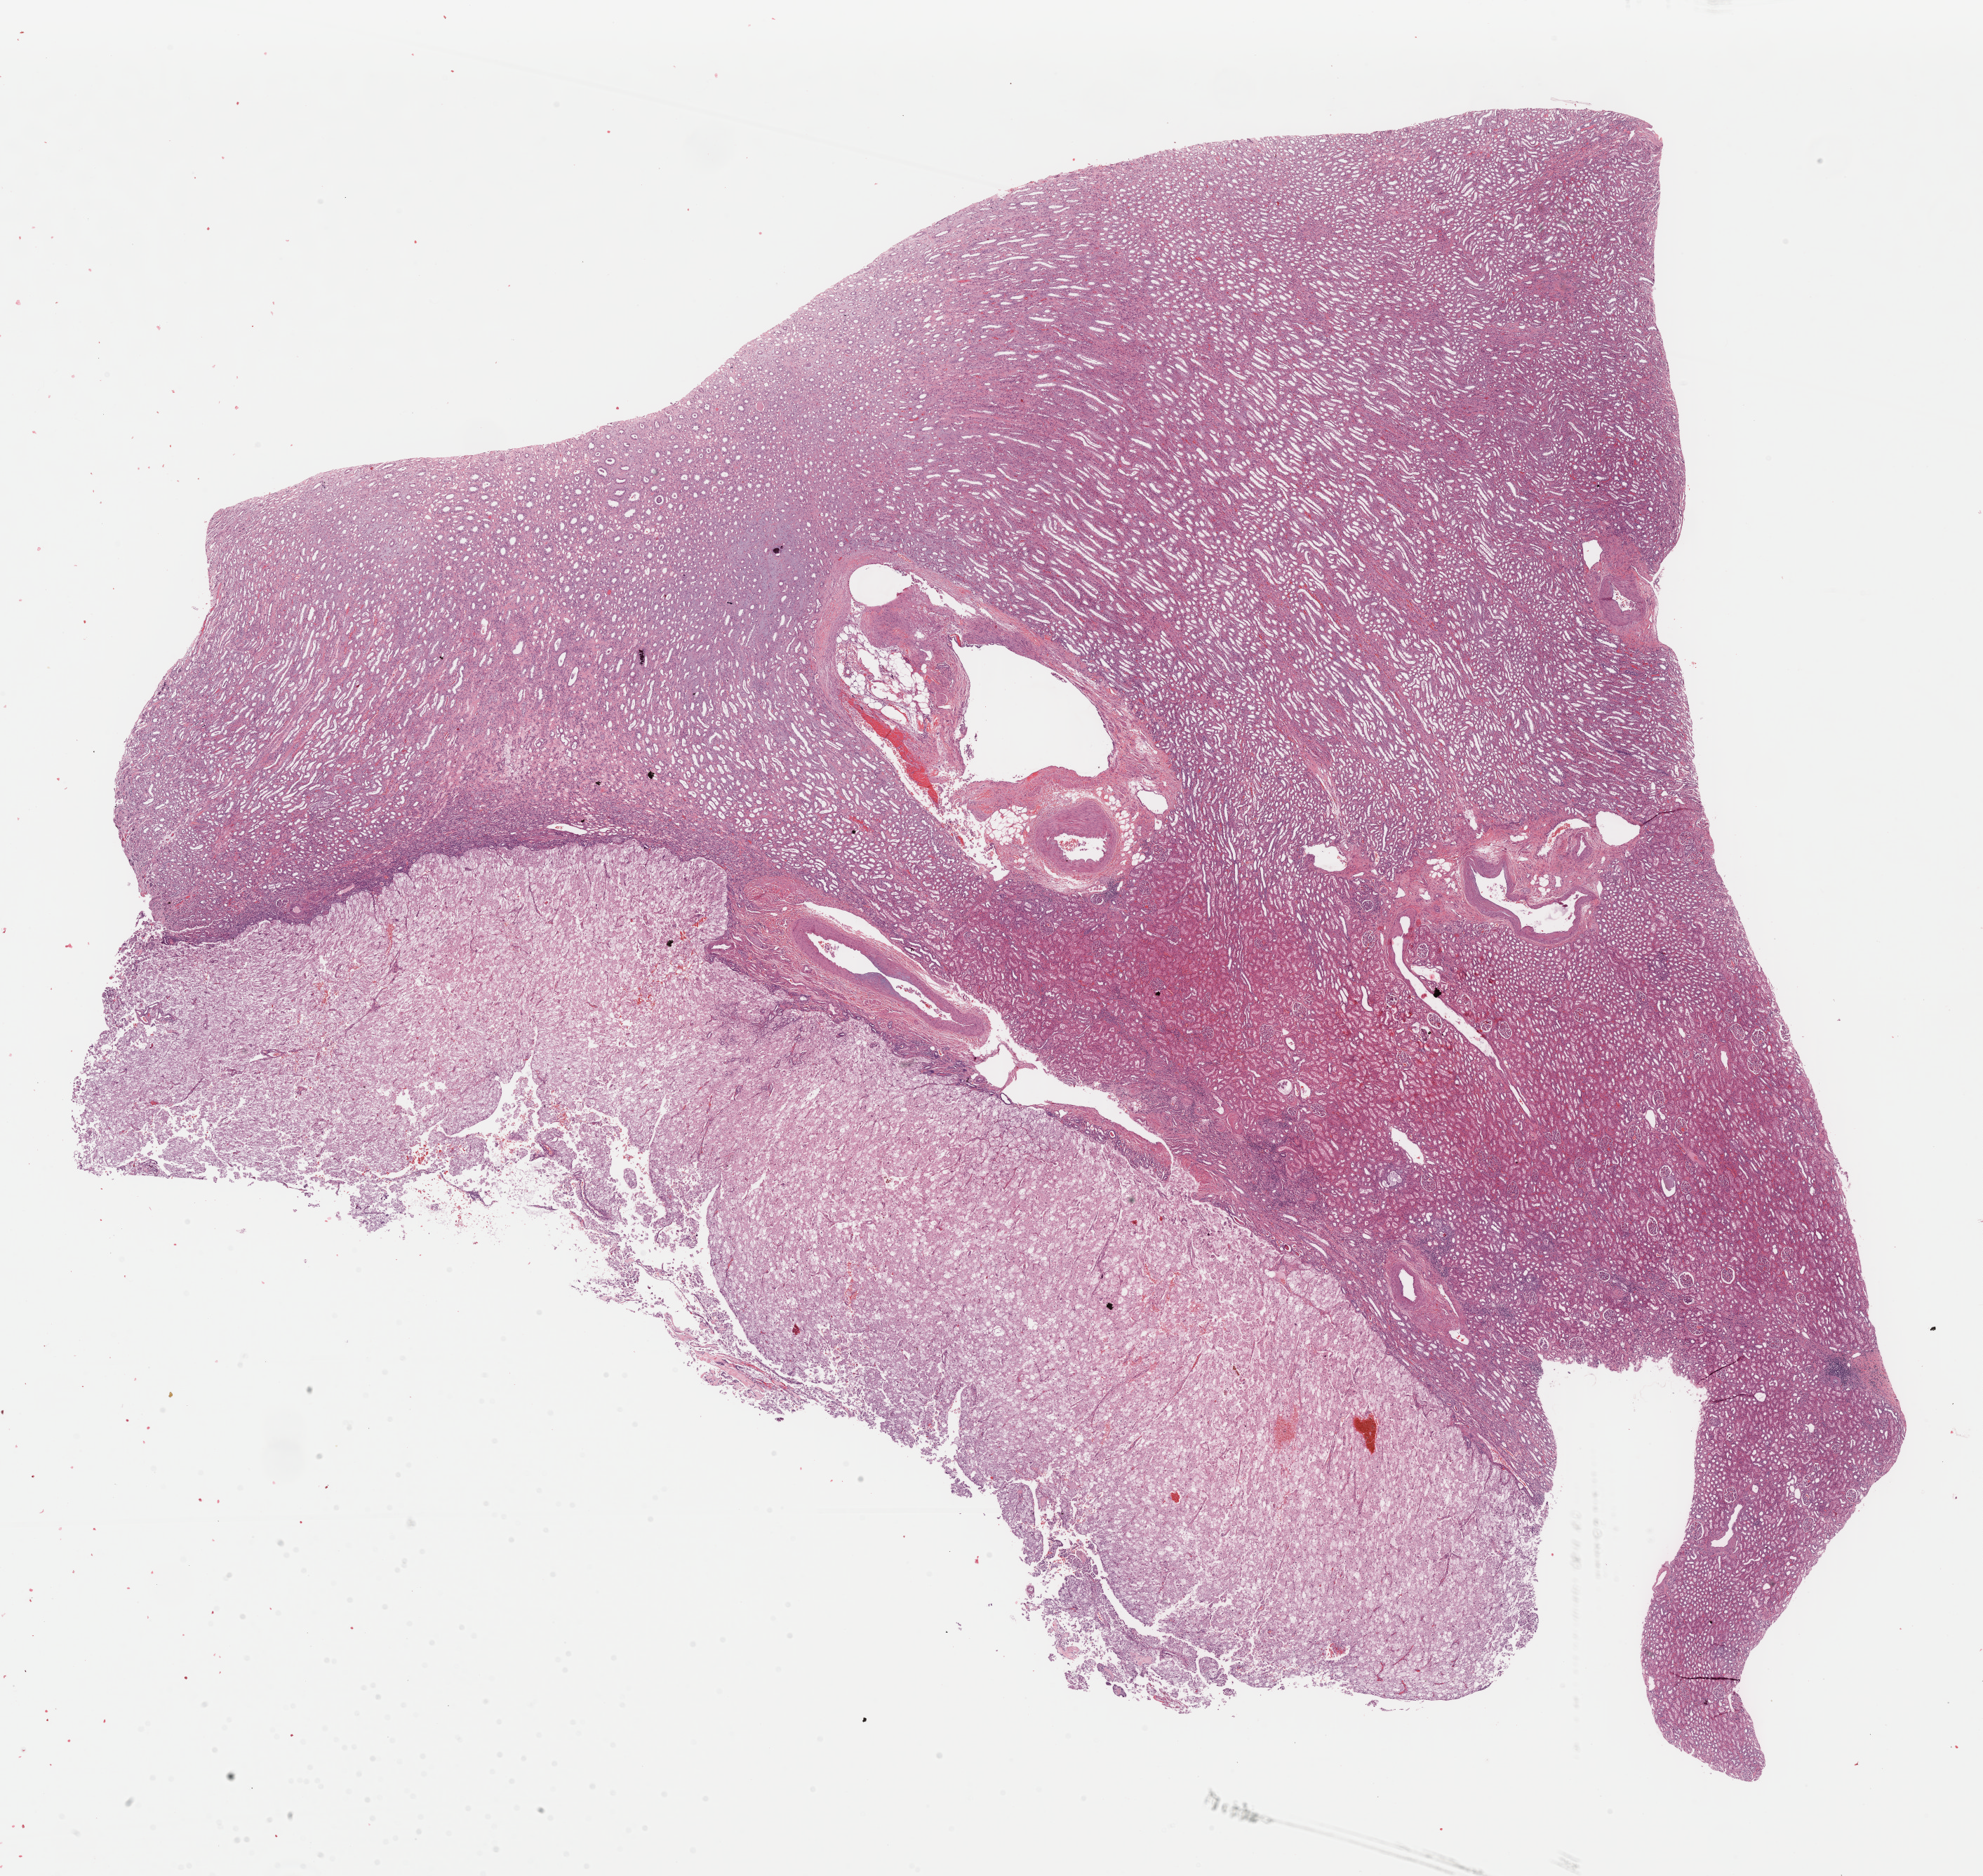
Digitized H&E tissue section (whole slide) — whole scanned area (about 22.3 x 21.1 mm) shown as a low-resolution overview, formalin-fixed paraffin-embedded (FFPE) diagnostic section, kidney, primary tumour sample. Male, age 49 years at initial diagnosis.
* histologic diagnosis: Renal cell carcinoma, chromophobe type
* TNM: T1a NX
* AJCC pathologic stage: I (7th edition)